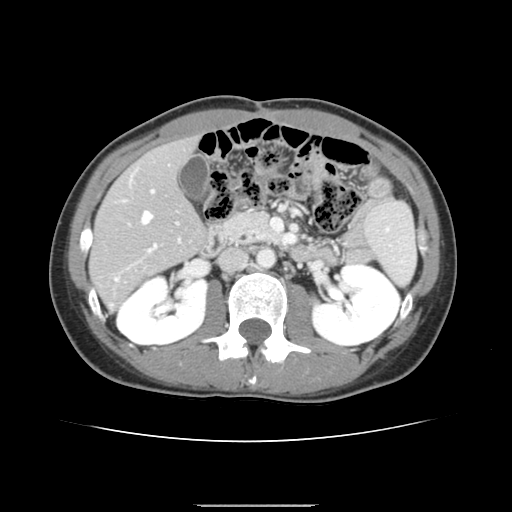
Contrast-enhanced abdominal CT, one axial slice; position 69 of 150 along the scan axis; 120 kVp; intravenous contrast given; soft-tissue window (W 400 / L 40 HU); 2.5 mm slice thickness; 512 × 512 image matrix, field of view 324 × 324 mm. Female patient, age 32 years. Case-level facts recorded for this patient, not image findings: diagnosis: colorectal cancer liver metastases, imaged before liver resection; multiple liver metastases: yes; largest metastasis: 0.7 cm; chemotherapy before resection: yes.
Structures marked on this image (expert manual segmentation):
- hepatic veins: box from (x=116, y=211) to (x=152, y=280) px
- liver: (x=91, y=140)–(x=203, y=307)
- planned liver remnant (the part of the liver to remain after resection): (x=91, y=140)–(x=203, y=287)
- portal vein (with intrahepatic branches): (x=111, y=177)–(x=180, y=305)